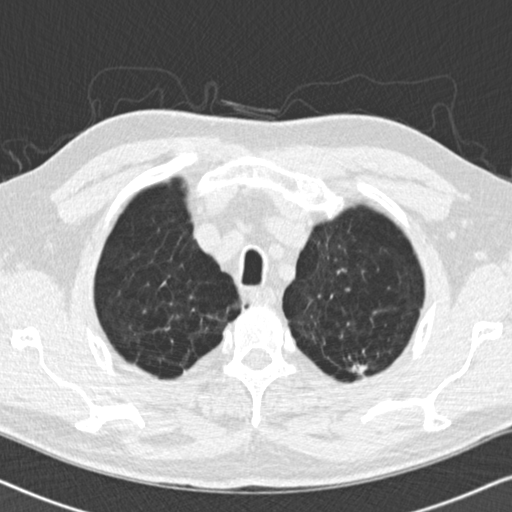
Low-dose screening chest CT, one axial slice. Slice 153 of 175 in the series (ordered by position). 120 kVp. Lung window (W 1500 / L -600 HU). 2 mm slice thickness. 512 × 512 image matrix, field of view 330 × 330 mm.
Outlined on this slice (expert manual segmentation):
- lesion 1 (tumor, upper lobe of left lung): bounding box <351,364,368,375> (left, top, right, bottom; pixels)